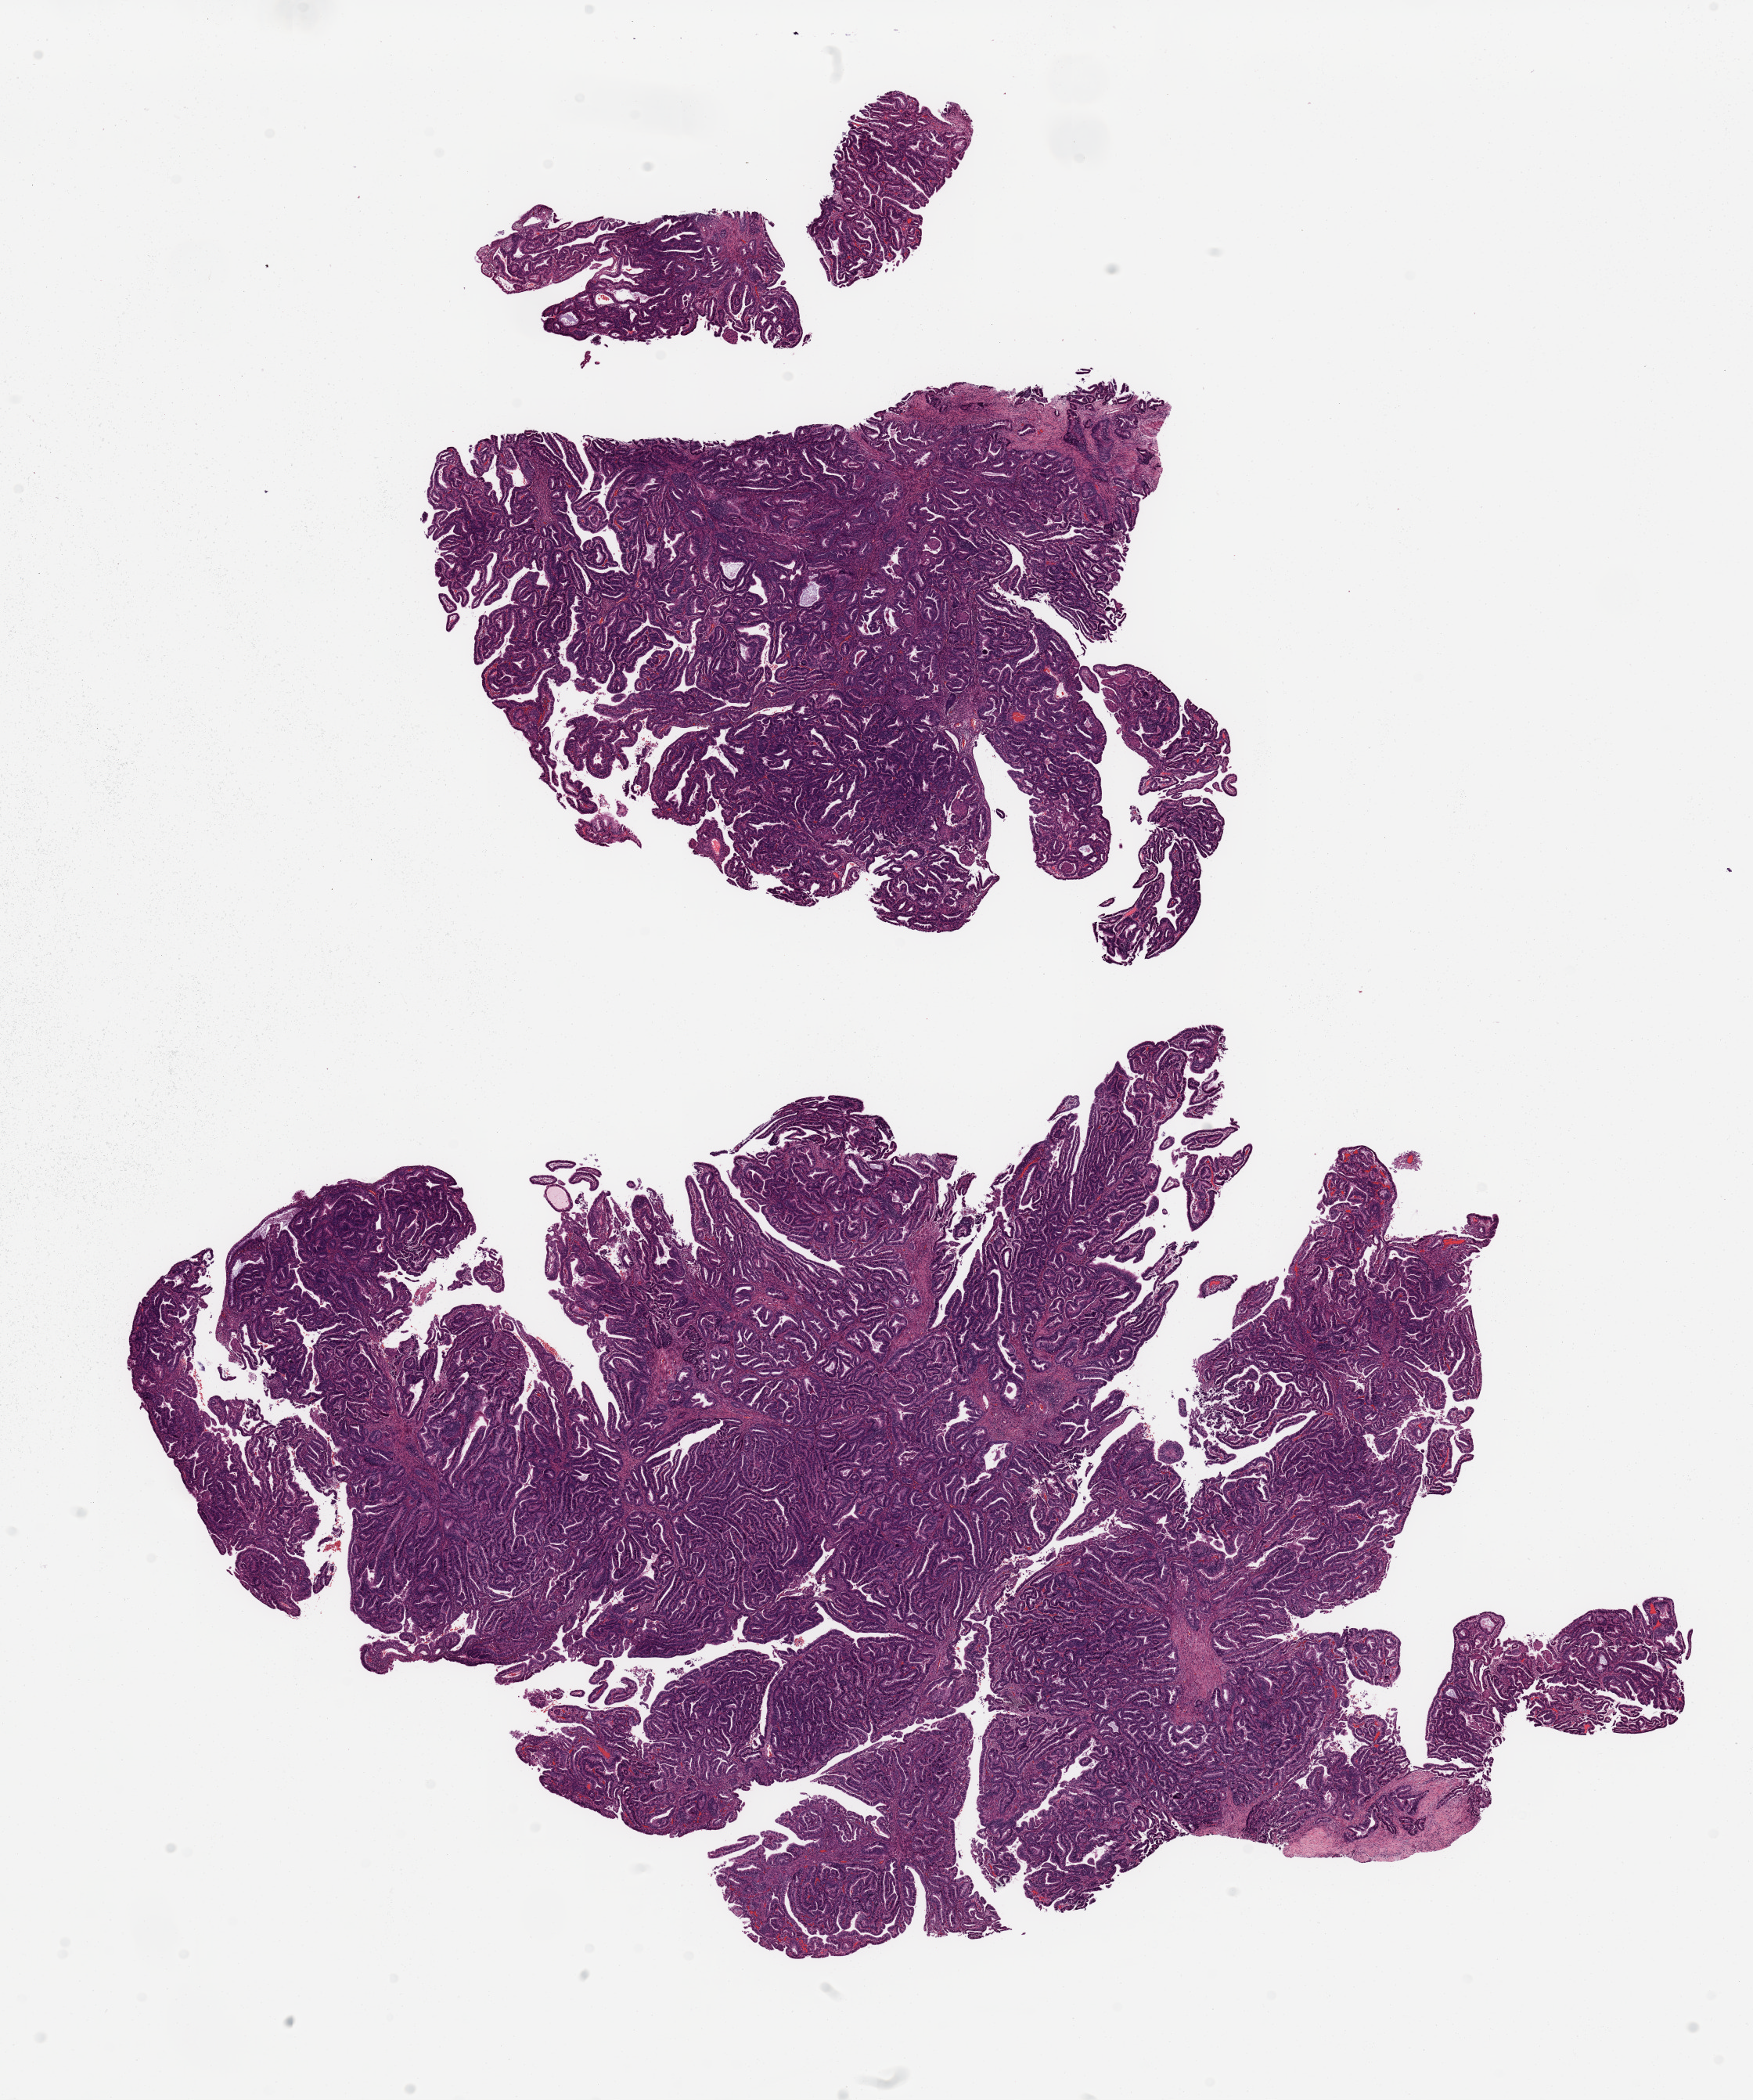
Whole-slide histology image, H&E-stained, a low-resolution overview of the entire scanned area, about 17.7 x 21.2 mm (slide scanned at 20x); tumour tissue sample, sampled site: uterus. 38-year-old female patient. Slide review estimates, as recorded: tumour nuclei 90%, necrosis 0%.
Diagnosis: Endometrioid adenocarcinoma, NOS.